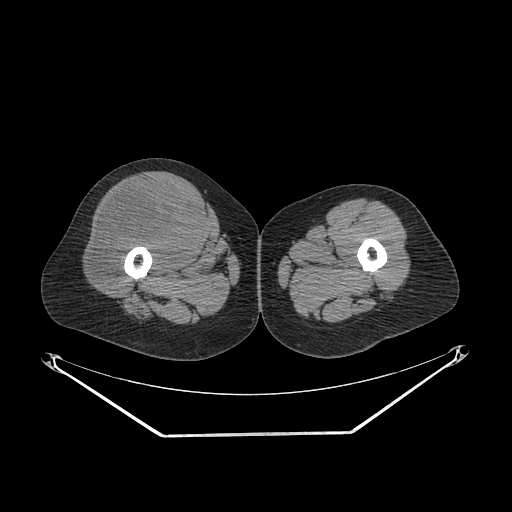
CT of an extremity soft-tissue mass (from a PET/CT study), one axial slice; slice 251 of 311 in the series (ordered by position); 140 kVp; soft-tissue window (W 400 / L 40 HU); 3.75 mm slice thickness; 512 × 512 image matrix, field of view 500 × 500 mm. Female patient. From the clinical record (not read from this slice): histological type: pleiomorphic undifferentiated sarcoma; grade: high; site of the primary tumour: right quadricep.
Annotated regions visible in this slice (expert contour drawn on MRI and transferred to this co-registered scan by the dataset authors):
- tumour plus oedema (research contour): bounding box [x1, y1, x2, y2] px = [93, 183, 200, 287]
- tumour (research contour): [93, 183, 200, 287]